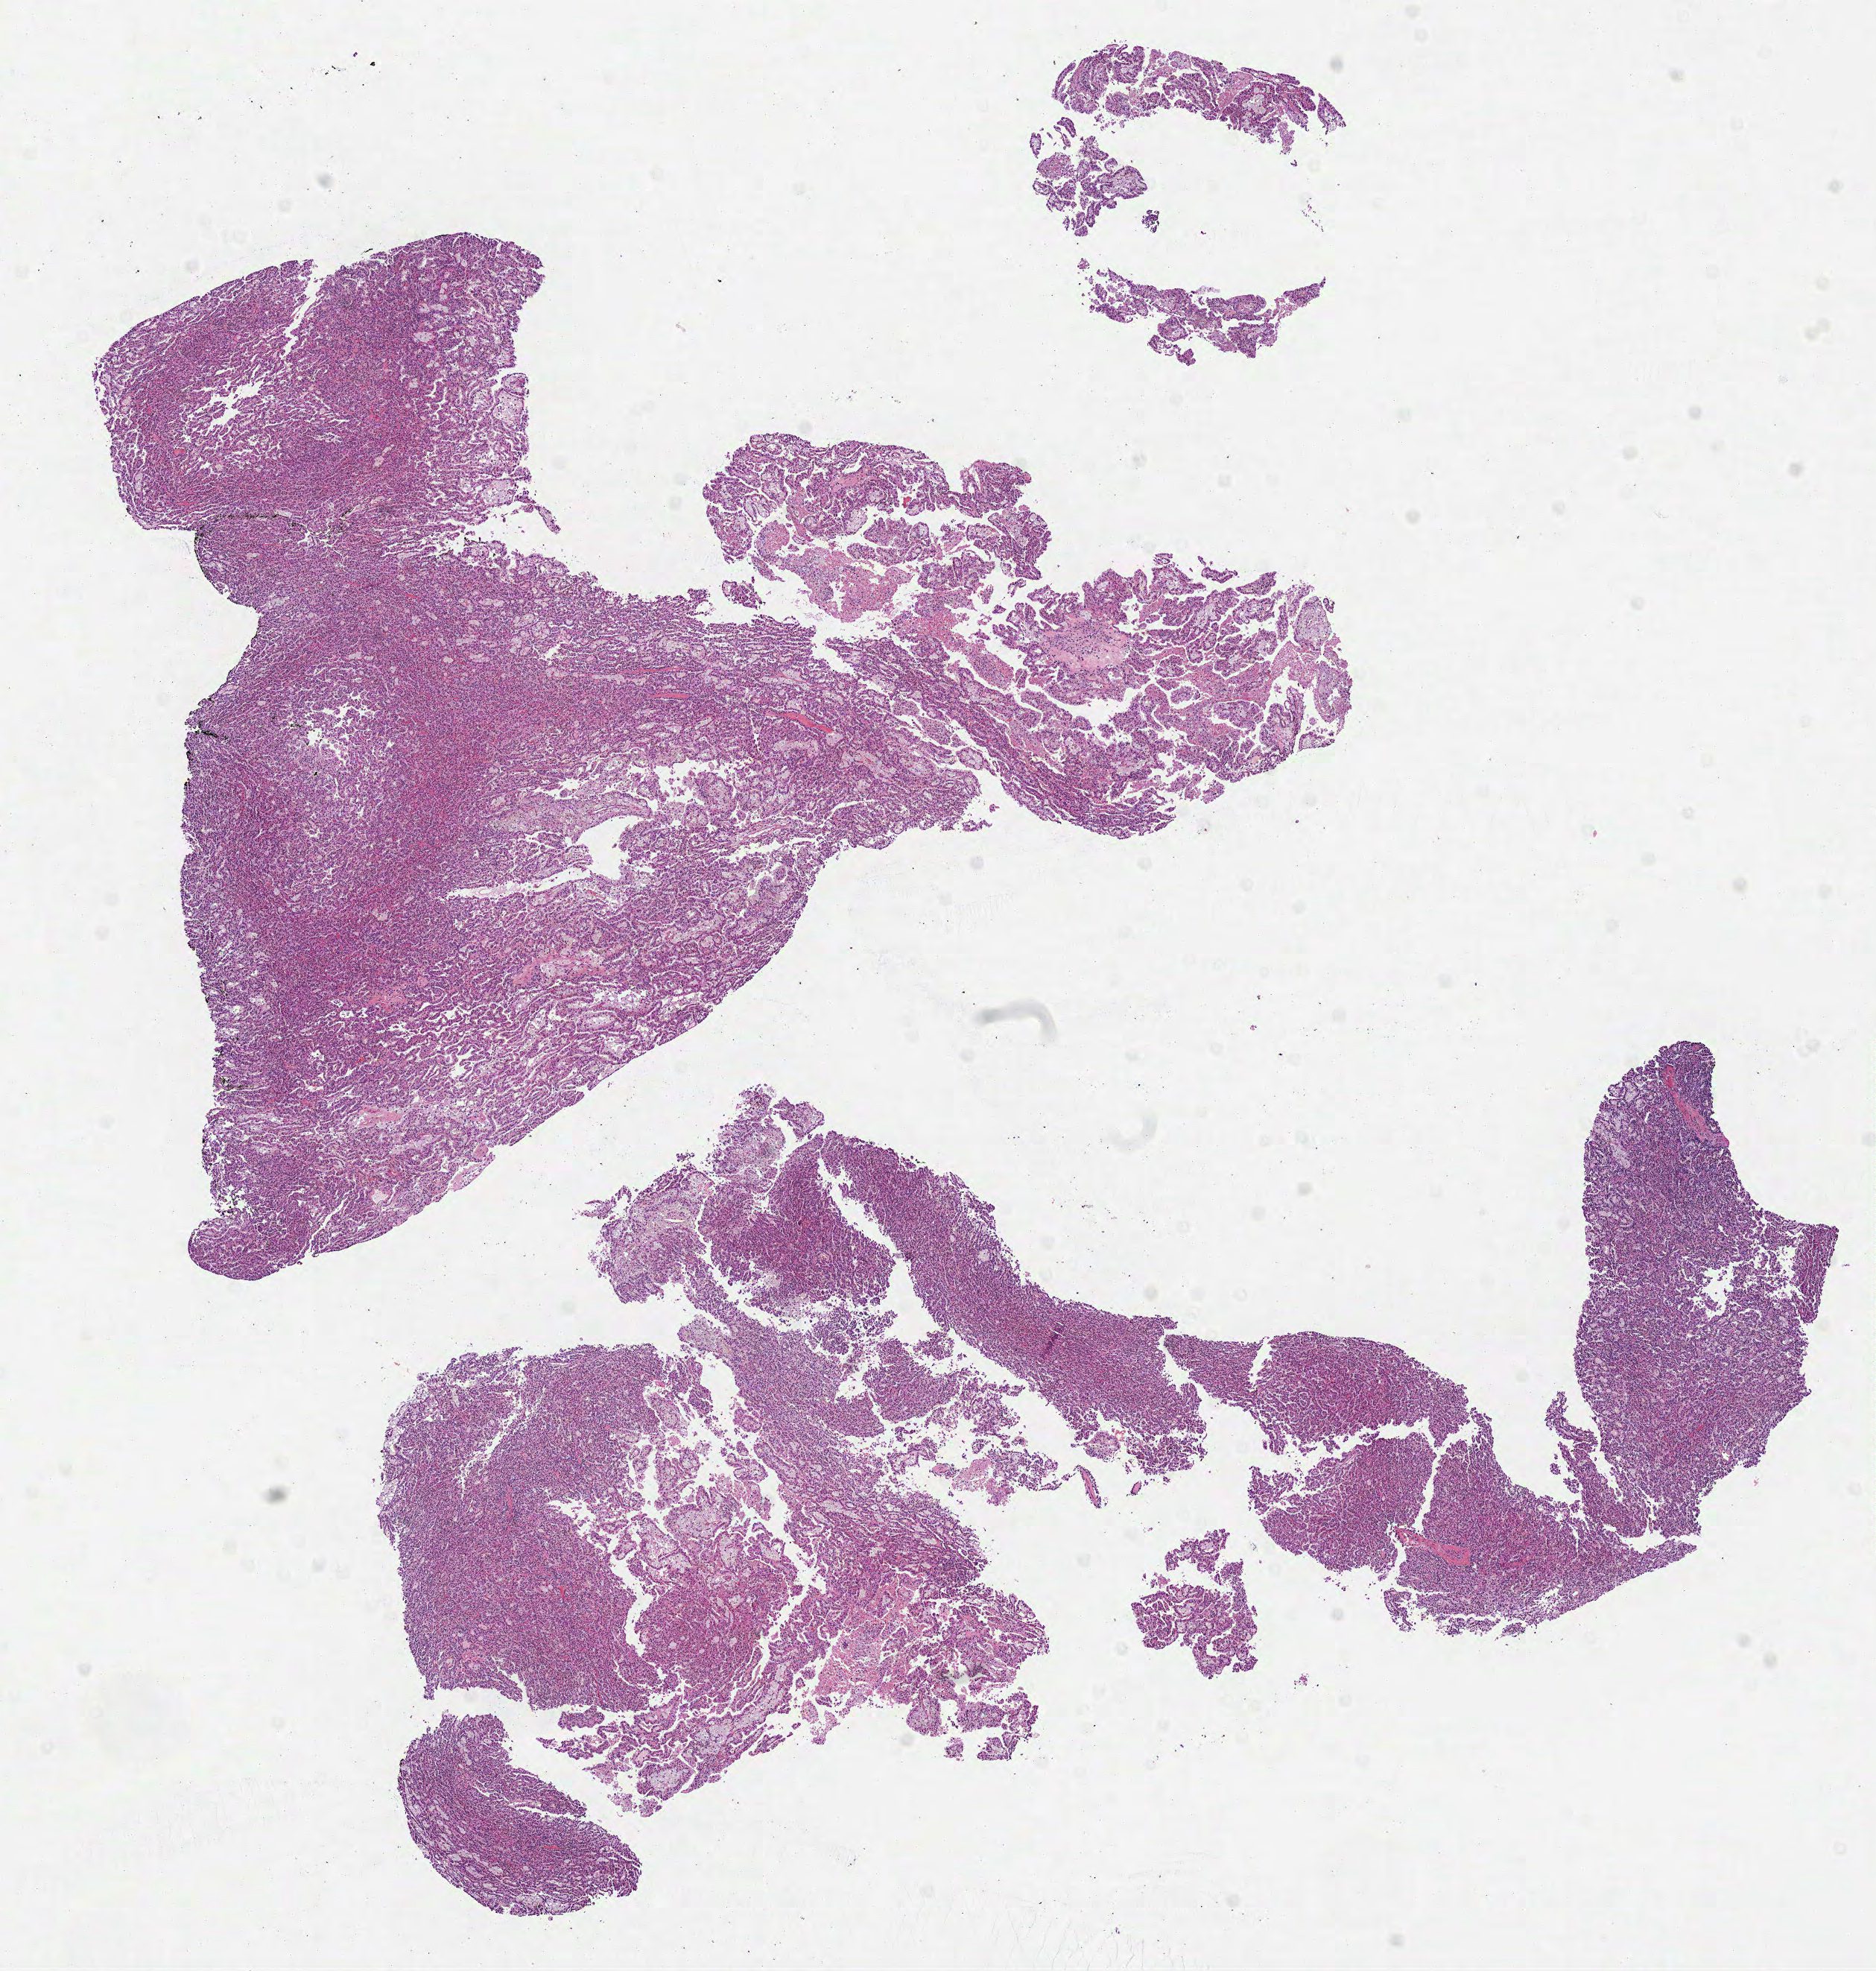
Hematoxylin and eosin (H&E) stained whole-slide image — a low-resolution overview of the entire scanned area, about 10.2 x 10.7 mm (from a 40x scan), formalin-fixed paraffin-embedded (FFPE) diagnostic section, kidney, primary tumour sample. Patient: male, age at initial diagnosis 55 years.
* laterality: right
* diagnosis: Papillary adenocarcinoma, NOS